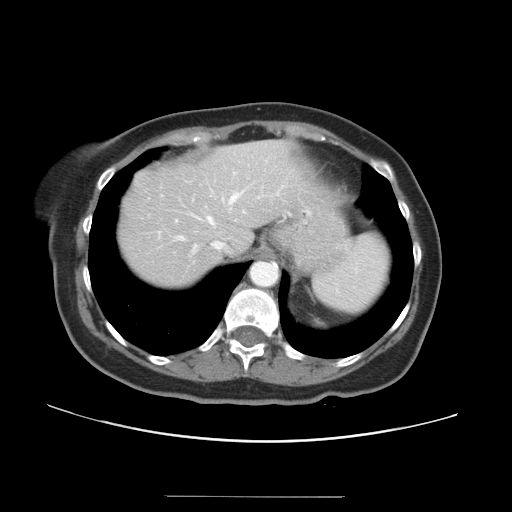
Contrast-enhanced abdominal CT, one axial slice. Position 28 of 34 along the scan axis. Reconstruction kernel STANDARD. 120 kVp. Intravenous contrast given. Soft-tissue window (W 400 / L 40 HU). 5 mm slice thickness. 512 × 512 image matrix, field of view 382 × 382 mm. Female patient, age 69 years. Case-level facts recorded for this patient, not image findings: diagnosis: colorectal cancer liver metastases, imaged before liver resection; multiple liver metastases: yes; largest metastasis: 1.4 cm.
Structures marked on this image (manually delineated by an expert):
- hepatic veins: box from (x=173, y=190) to (x=245, y=254) px
- liver: (x=120, y=140)–(x=305, y=288)
- planned liver remnant (the part of the liver to remain after resection): (x=120, y=140)–(x=305, y=288)